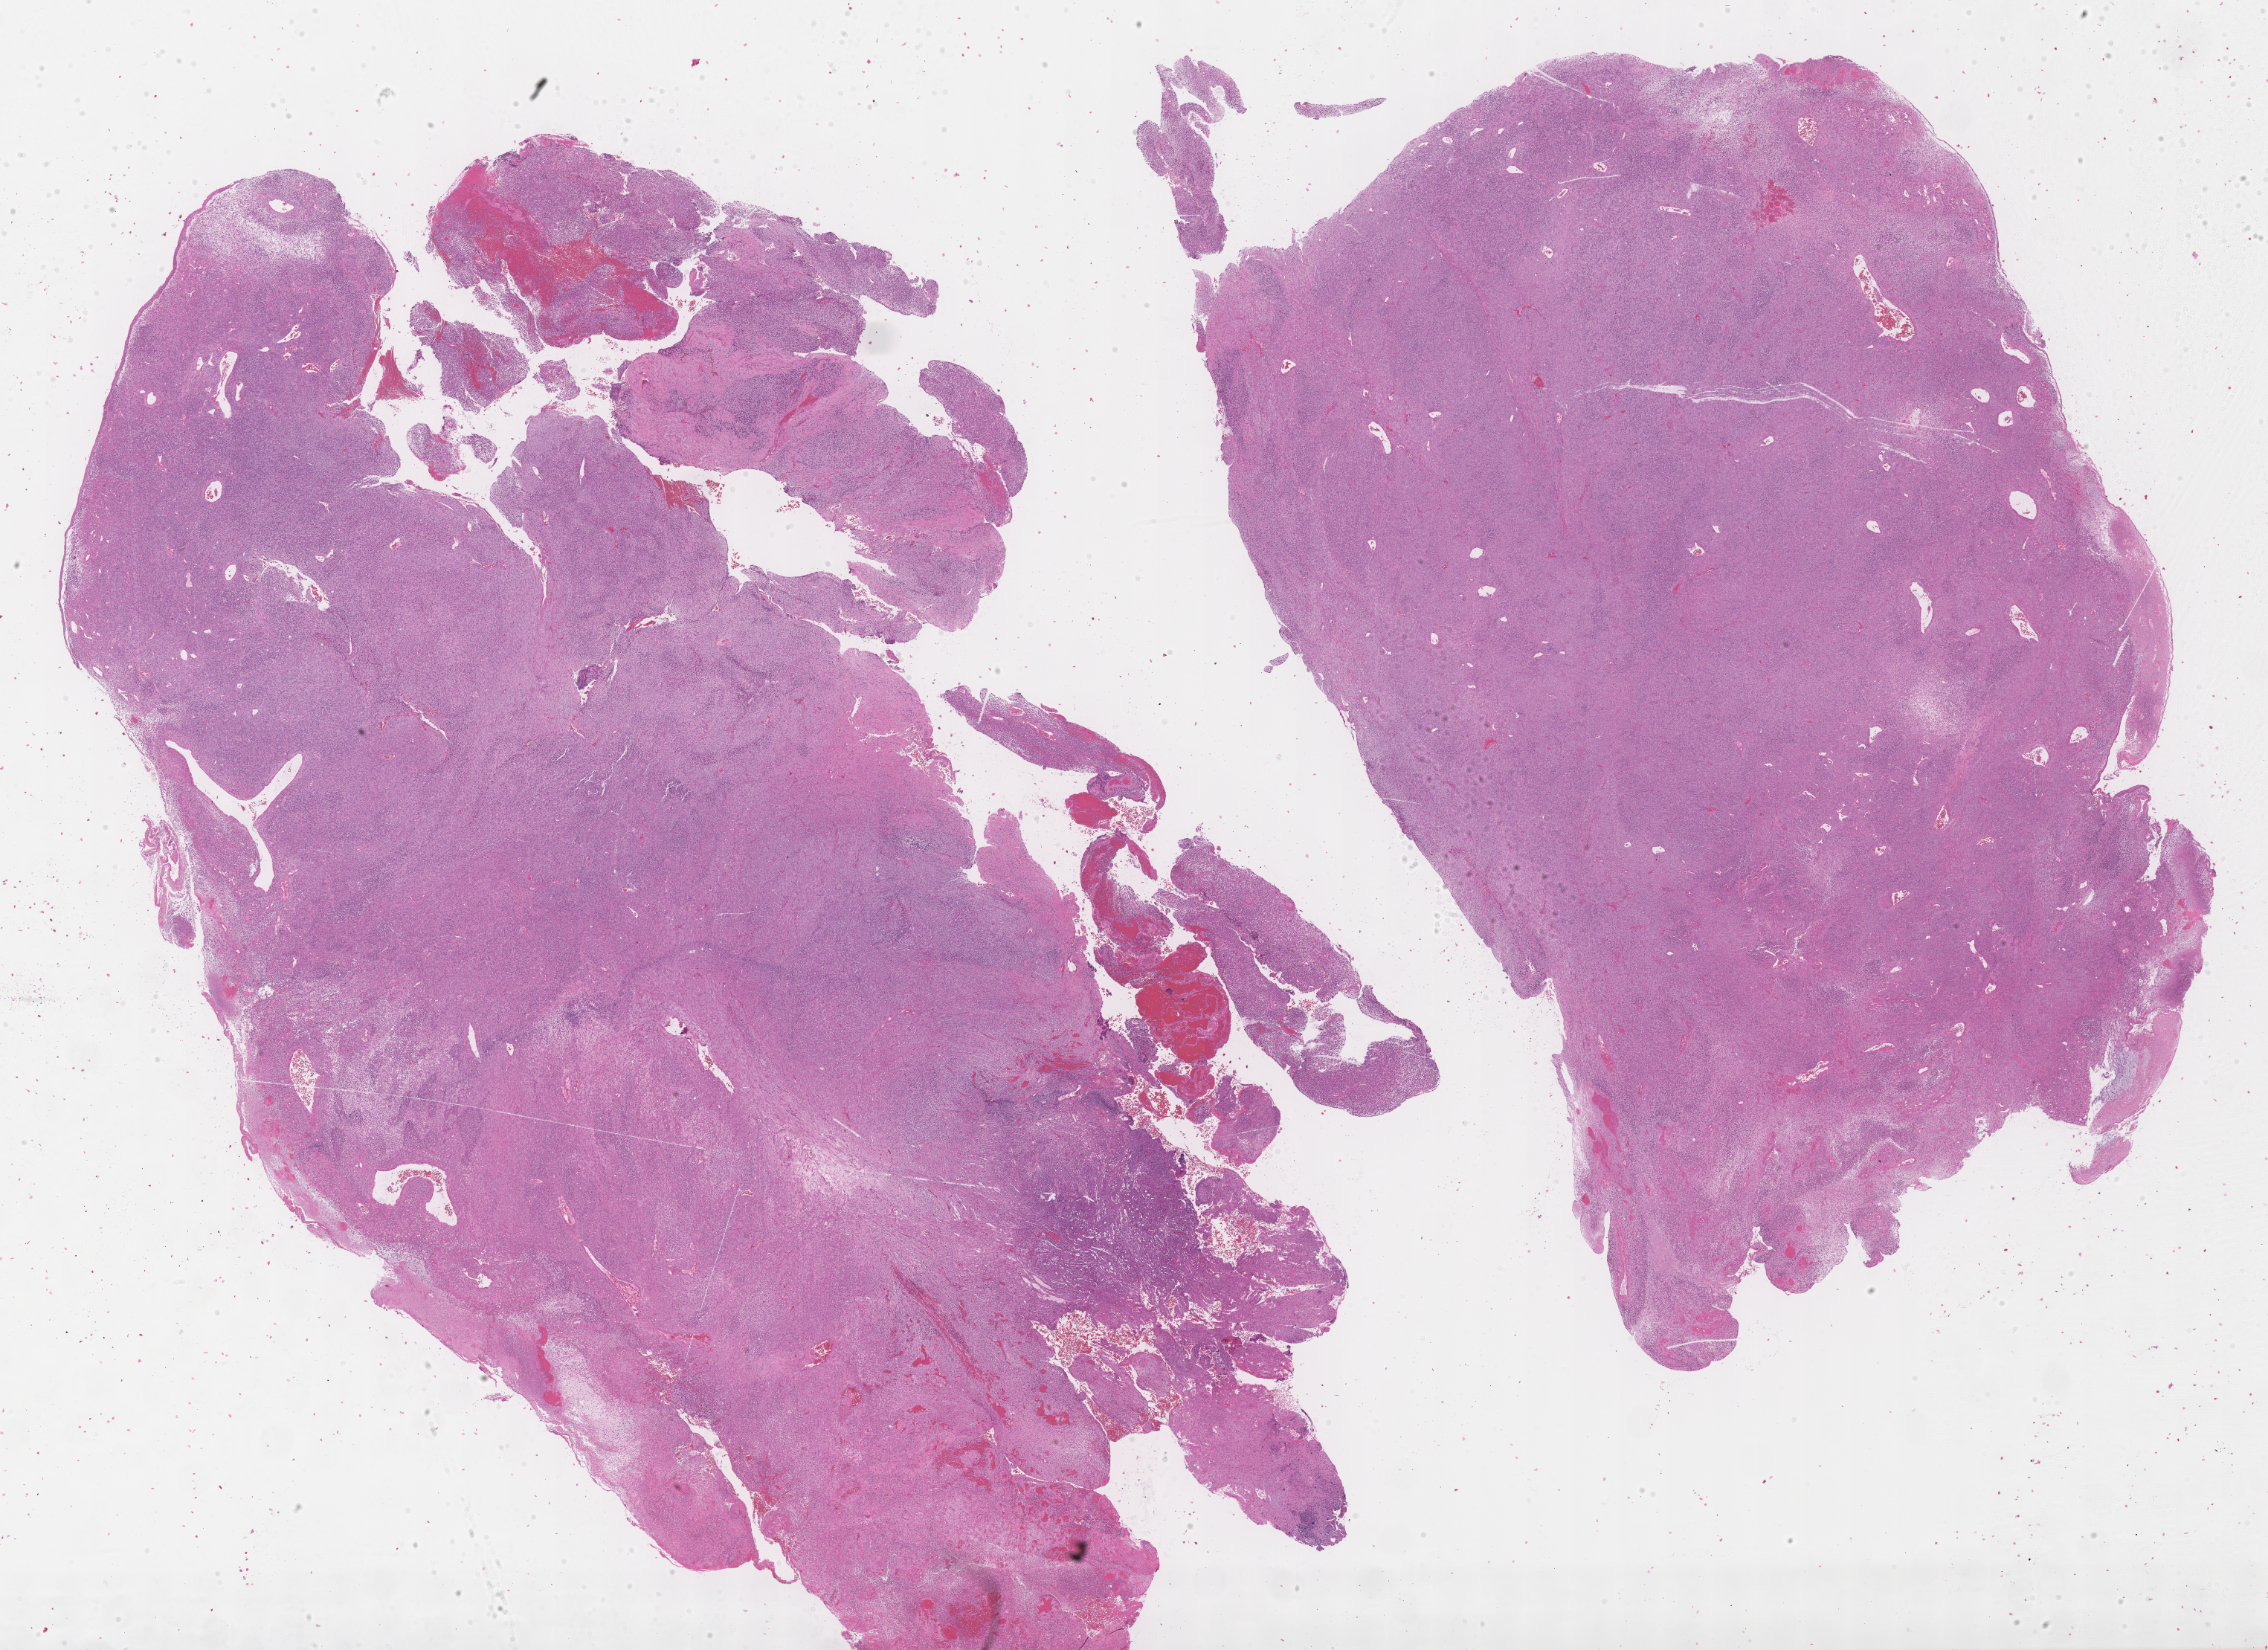
Whole-slide image, haematoxylin and eosin stain of tumor tissue, a low-resolution overview of the entire scanned area, about 24.7 x 17.9 mm. Formalin-fixed, paraffin-embedded (FFPE) tissue. Site: nasopharynx. Patient: male, age 7.5 years at diagnosis.
Diagnosis: rhabdomyosarcoma; histological classification: embryonal rhabdomyosarcoma.